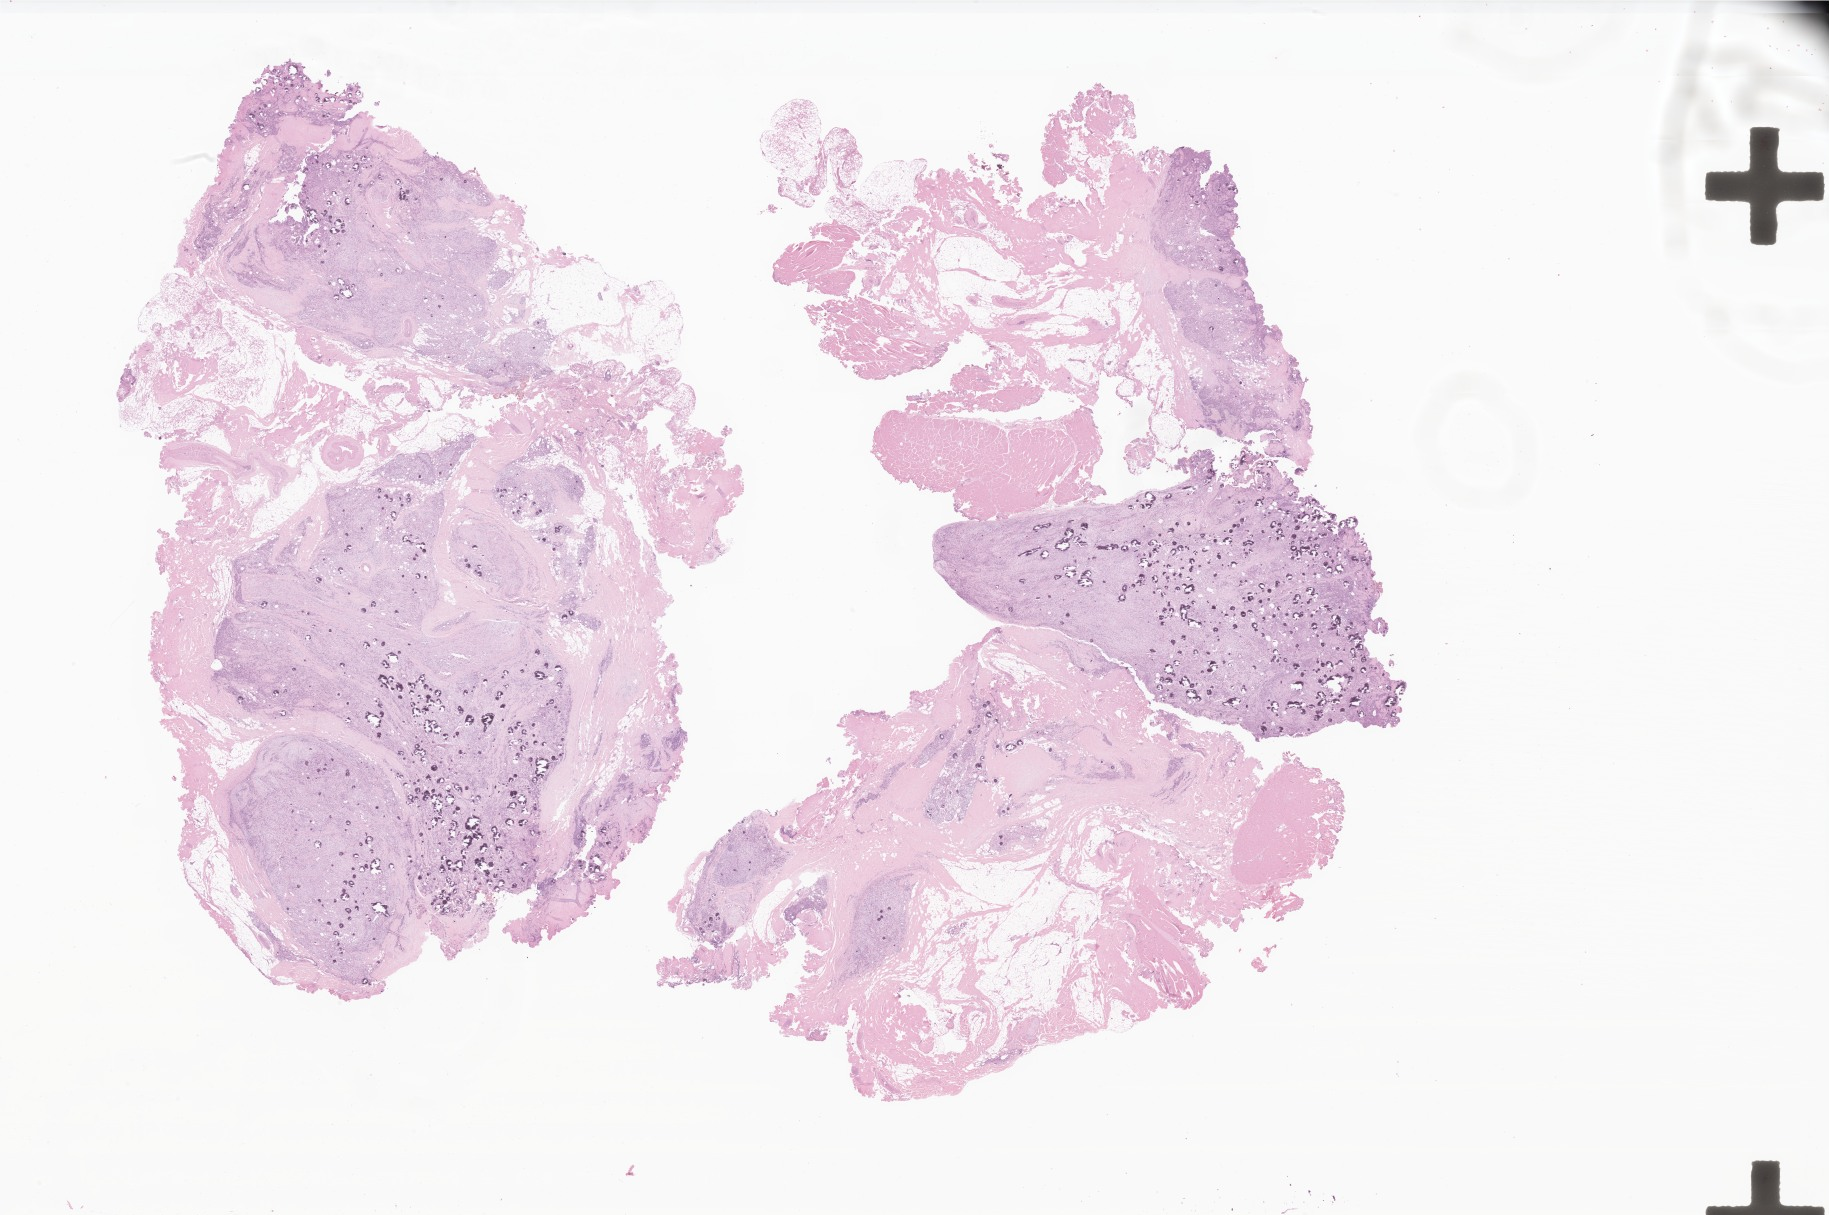
Digitized haematoxylin and eosin-stained section of tumor tissue from the brain, a low-resolution overview of the entire scanned area, about 30.8 x 20.5 mm. Formalin-fixed paraffin-embedded section. Patient: male, age 175 months (14 years 7 months).
Diagnosis: Meningioma, NOS.